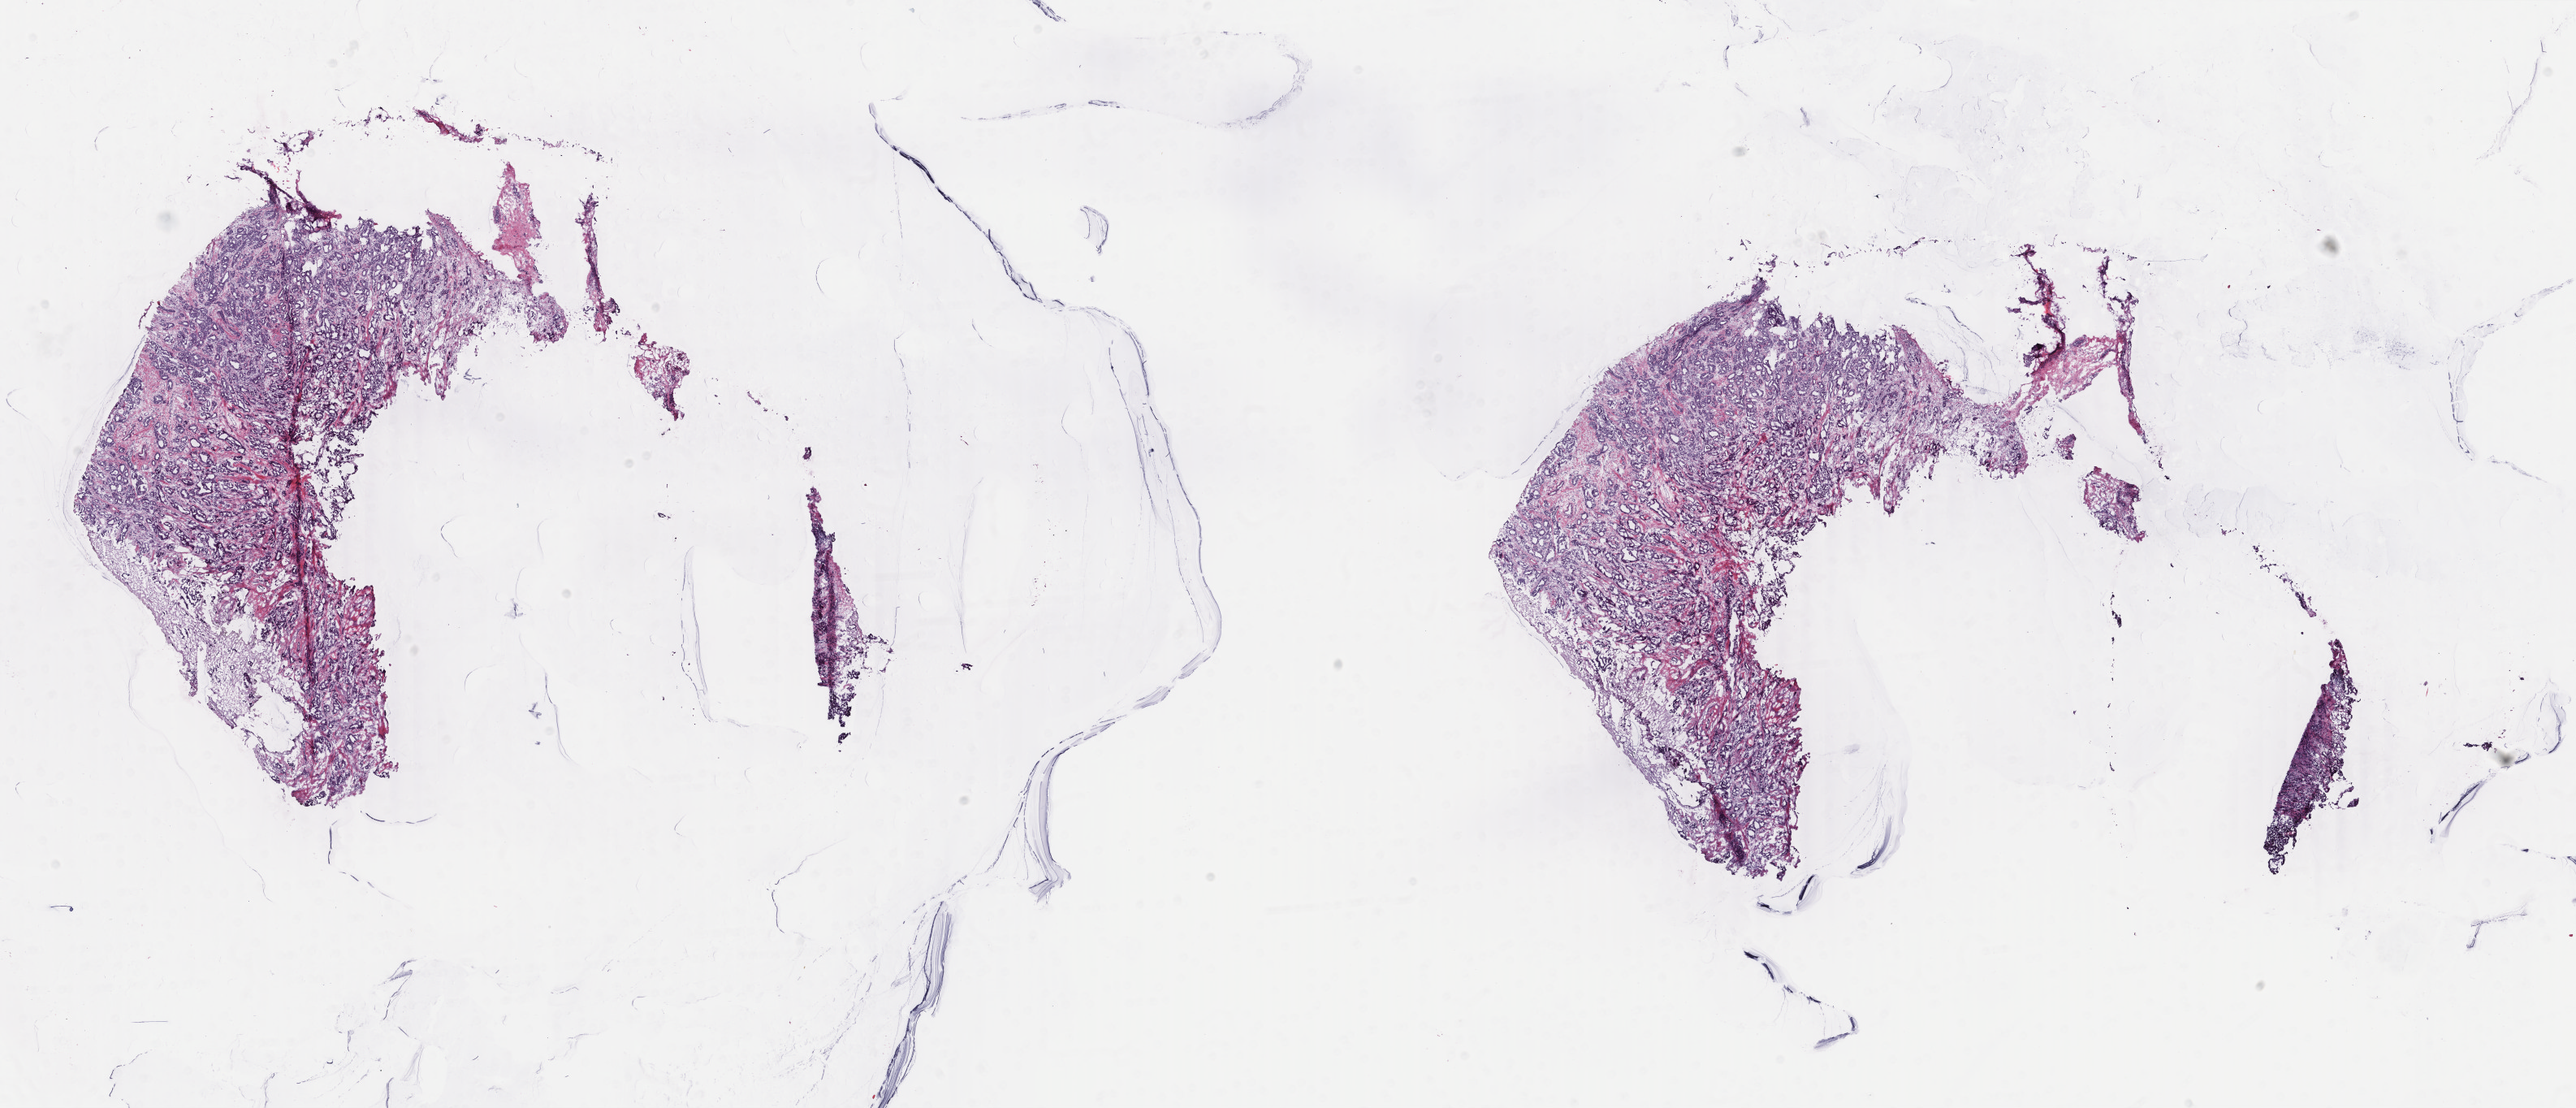
Whole-slide histology image, Hematoxylin and eosin (H&E) stained, shown as a low-resolution overview of the whole scanned area (about 25.2 x 10.8 mm), frozen section from the bottom of the tissue portion, sample: primary tumour, breast. Patient: female, age at initial diagnosis 79 years.
Diagnosis: Infiltrating duct carcinoma, NOS.